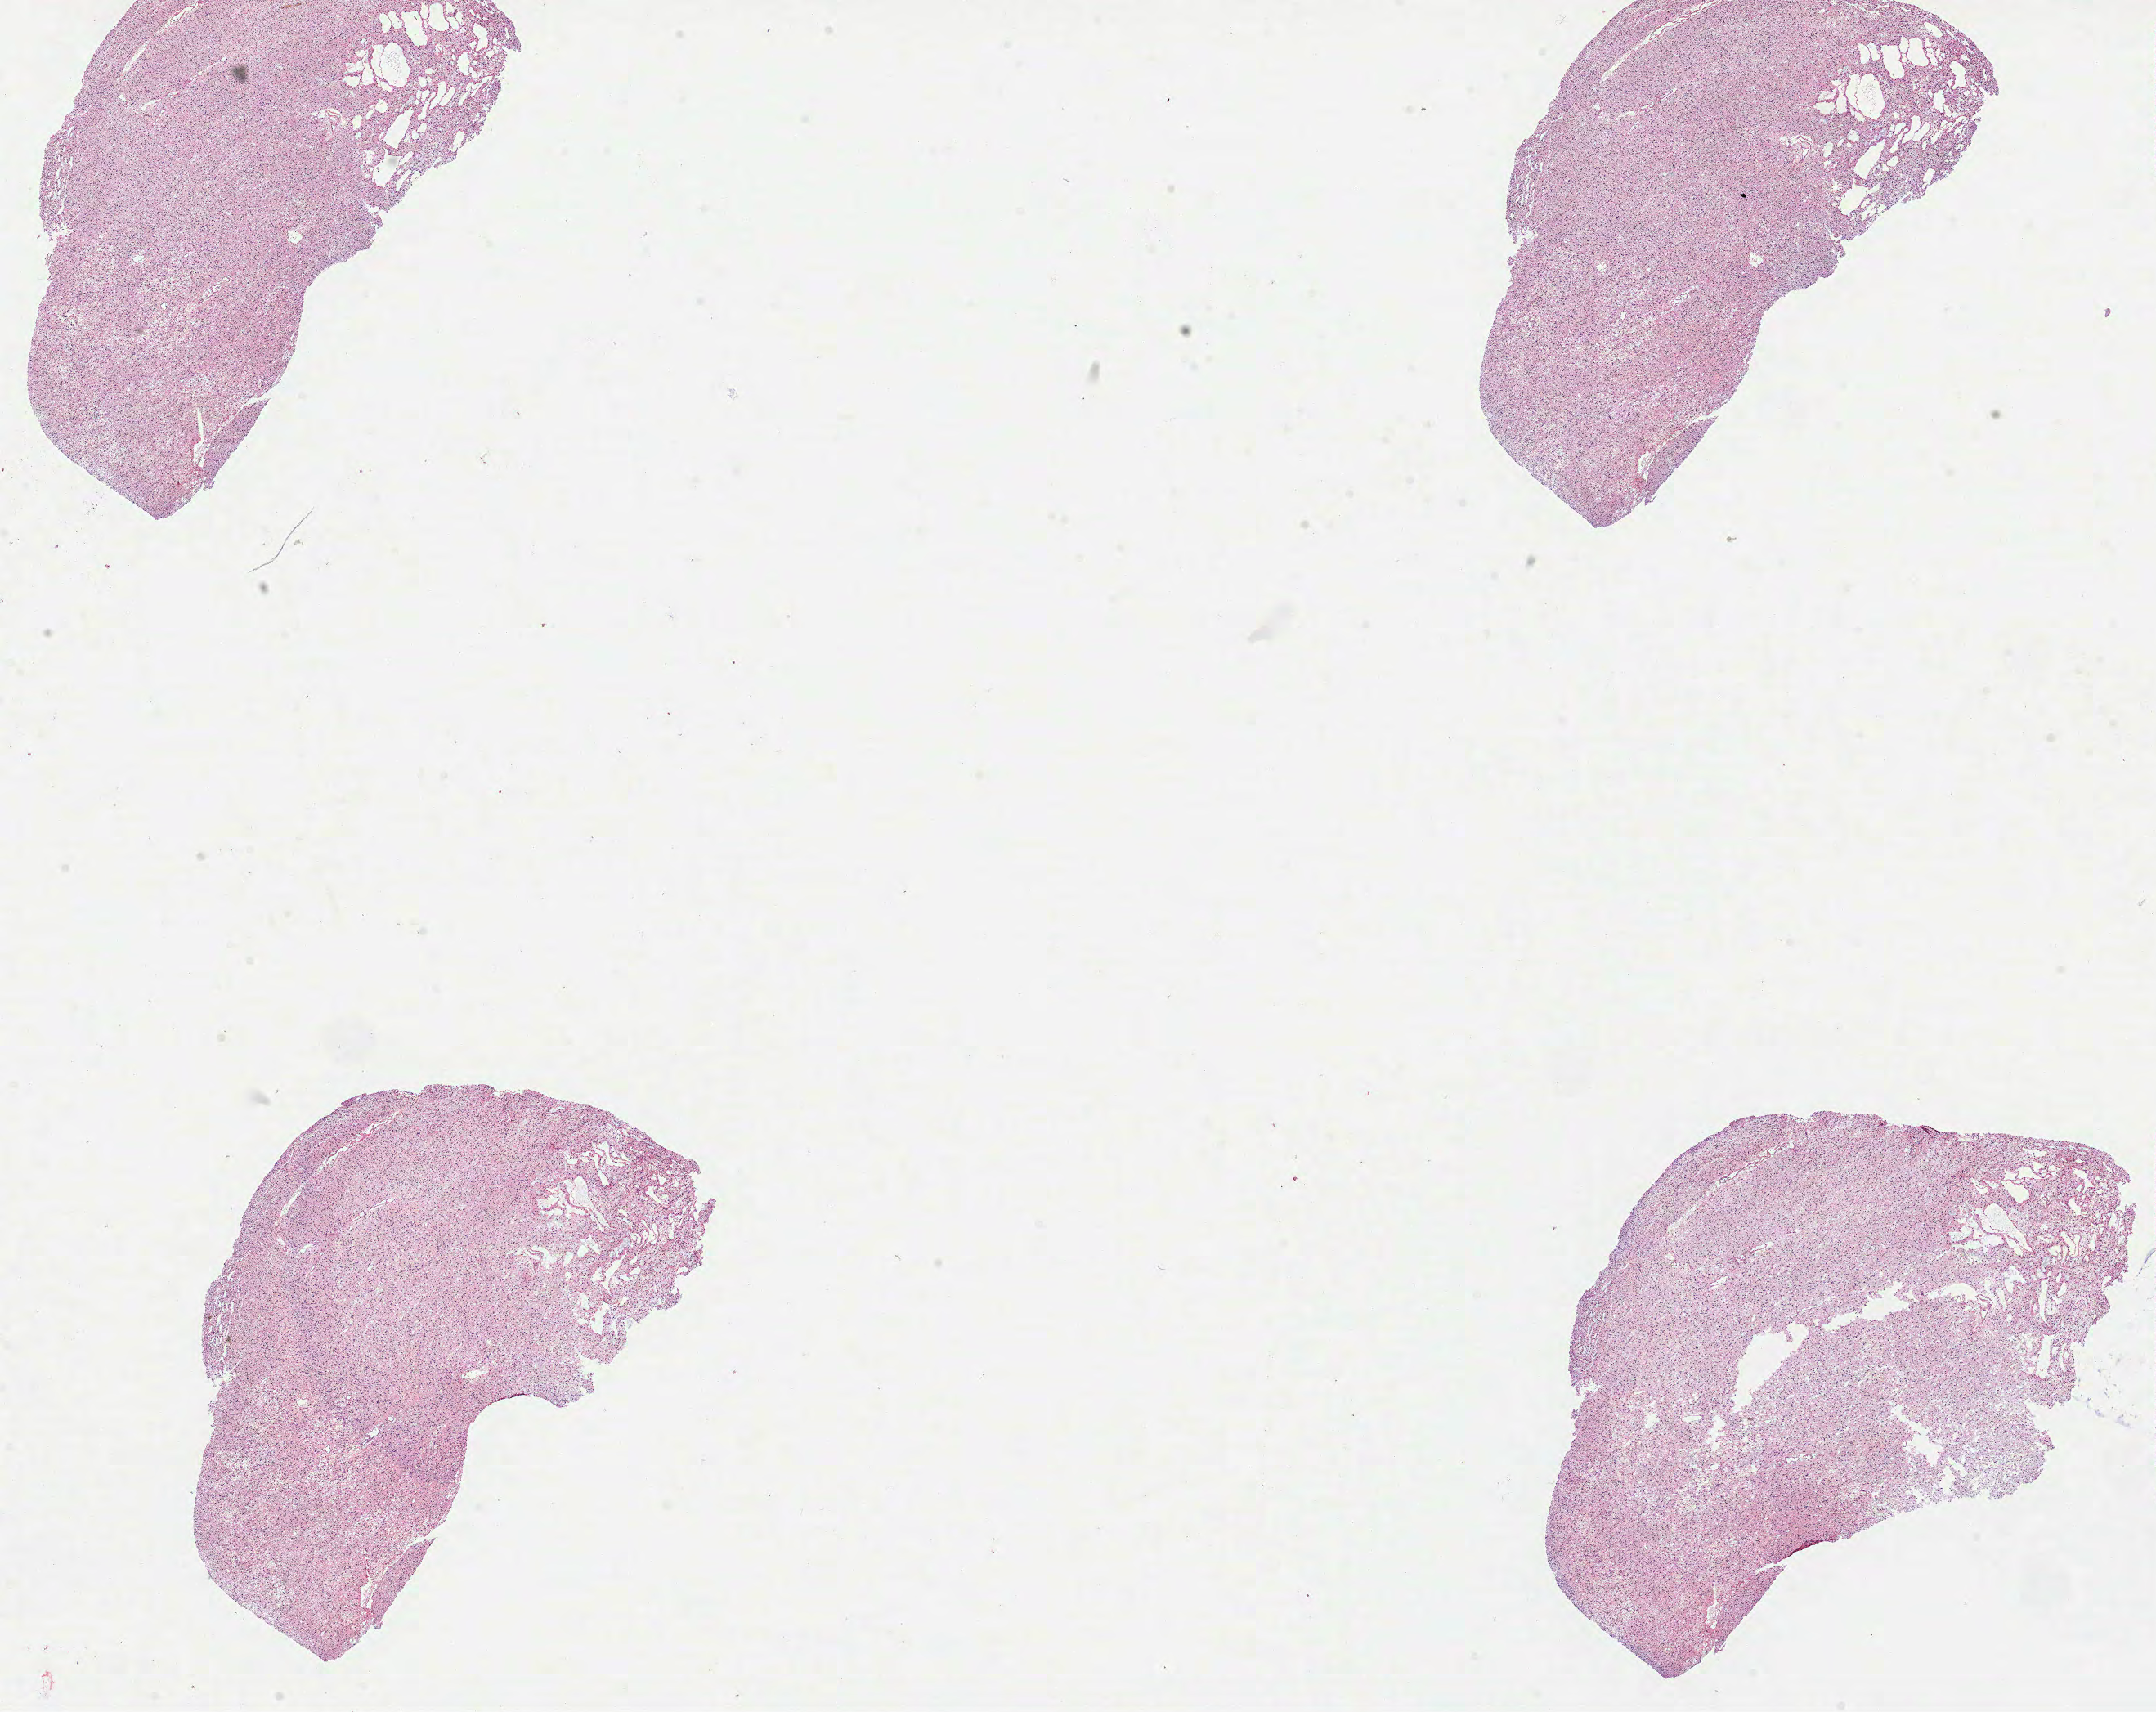
Whole-slide histology image, Hematoxylin and eosin (H&E) stained, low-resolution overview of the scanned area, about 21.3 x 16.9 mm (from a 40x scan). Formalin-fixed paraffin-embedded (FFPE) diagnostic section. Primary tumour sample from the brain. Patient: female, age at initial diagnosis 35 years.
Histologic diagnosis: Oligodendroglioma, NOS (cerebrum).